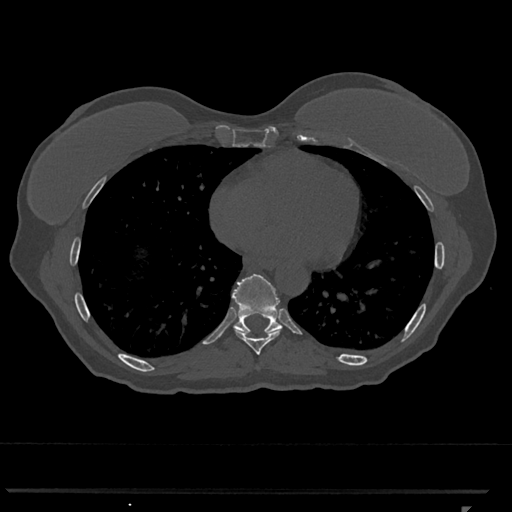
CT including the spine, one axial slice. Slice 645 of 793 in the series (ordered by position). Reconstruction kernel Br40s/3. Bone window (W 1800 / L 400 HU). 0.5 mm slice thickness. 512 × 512 image matrix, field of view 380 × 380 mm. Female patient, age 62 years. From the clinical record (not read from this slice): primary cancer: renal.
Structures marked on this image (semi-automatically segmented with operator editing):
- T8 vertebra: bounding box [x1, y1, x2, y2] px = [236, 330, 281, 355]
- T9 vertebra: [233, 274, 283, 334]